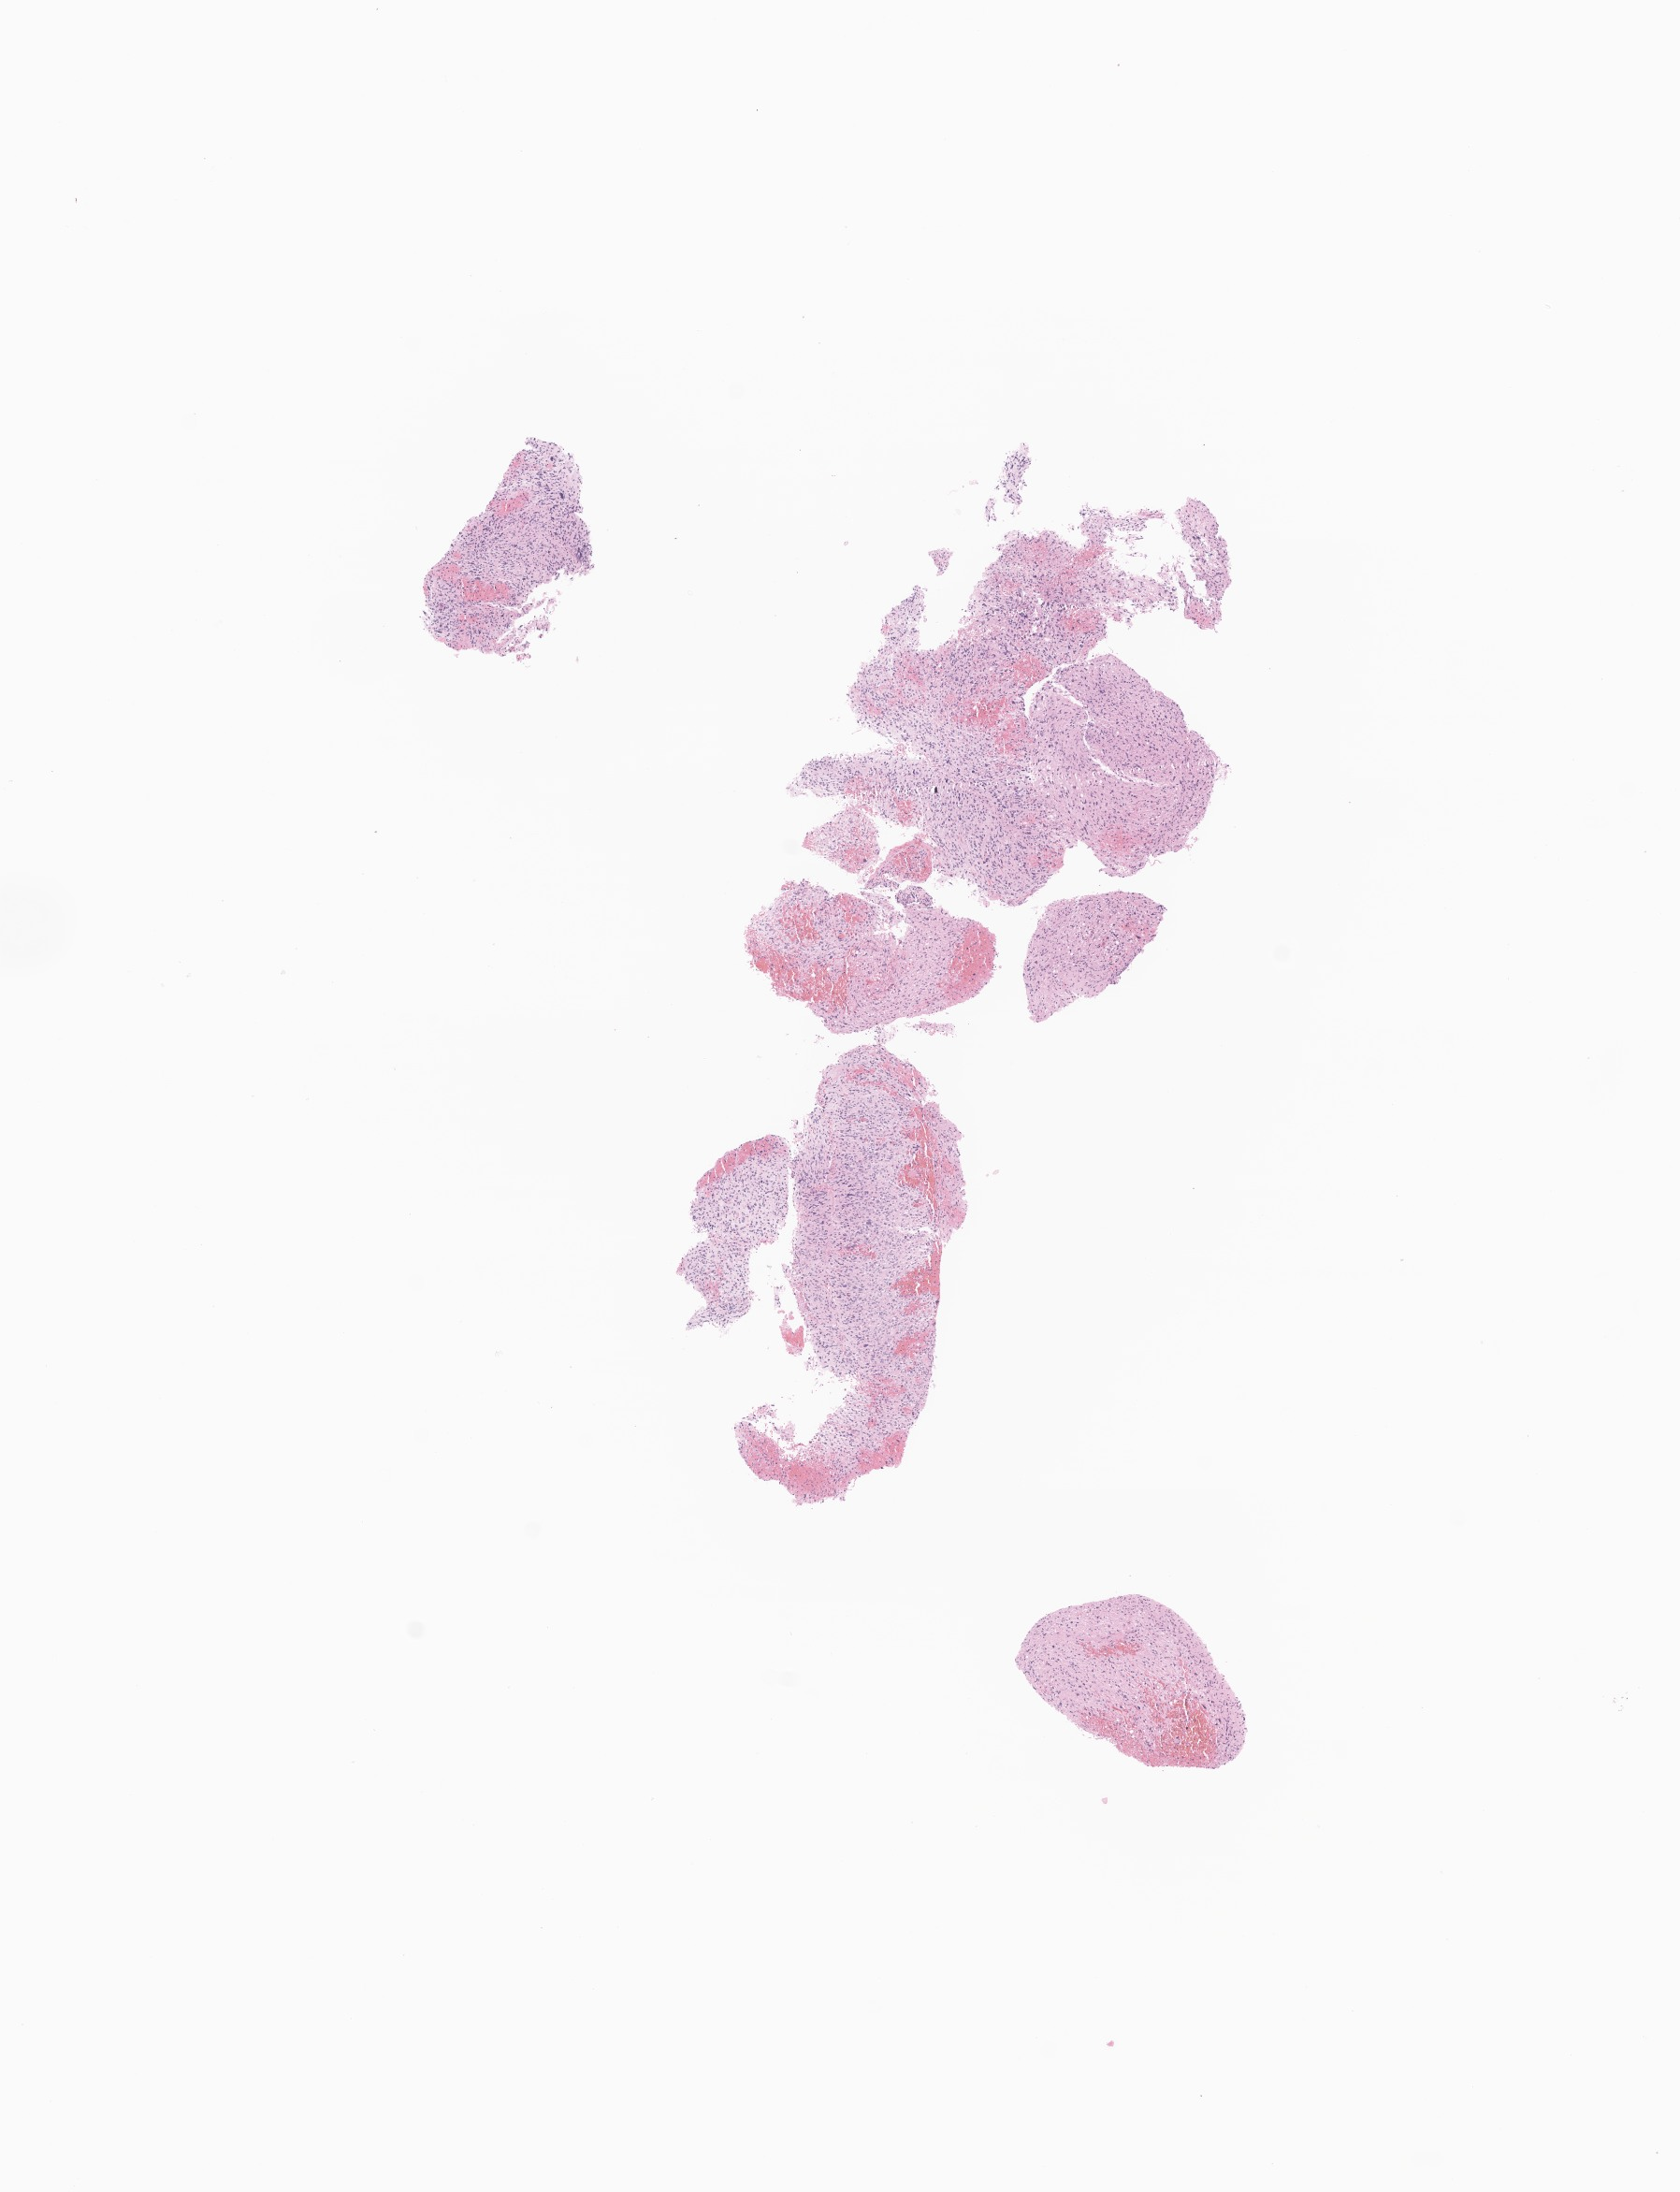
H&E whole-slide image of tumor tissue from the spinal cord — low-resolution overview of the scanned area, about 7.6 x 9.9 mm; formalin-fixed paraffin-embedded section. Patient: female, age 101 months (8 years 5 months).
Diagnosis: Glioma, malignant.